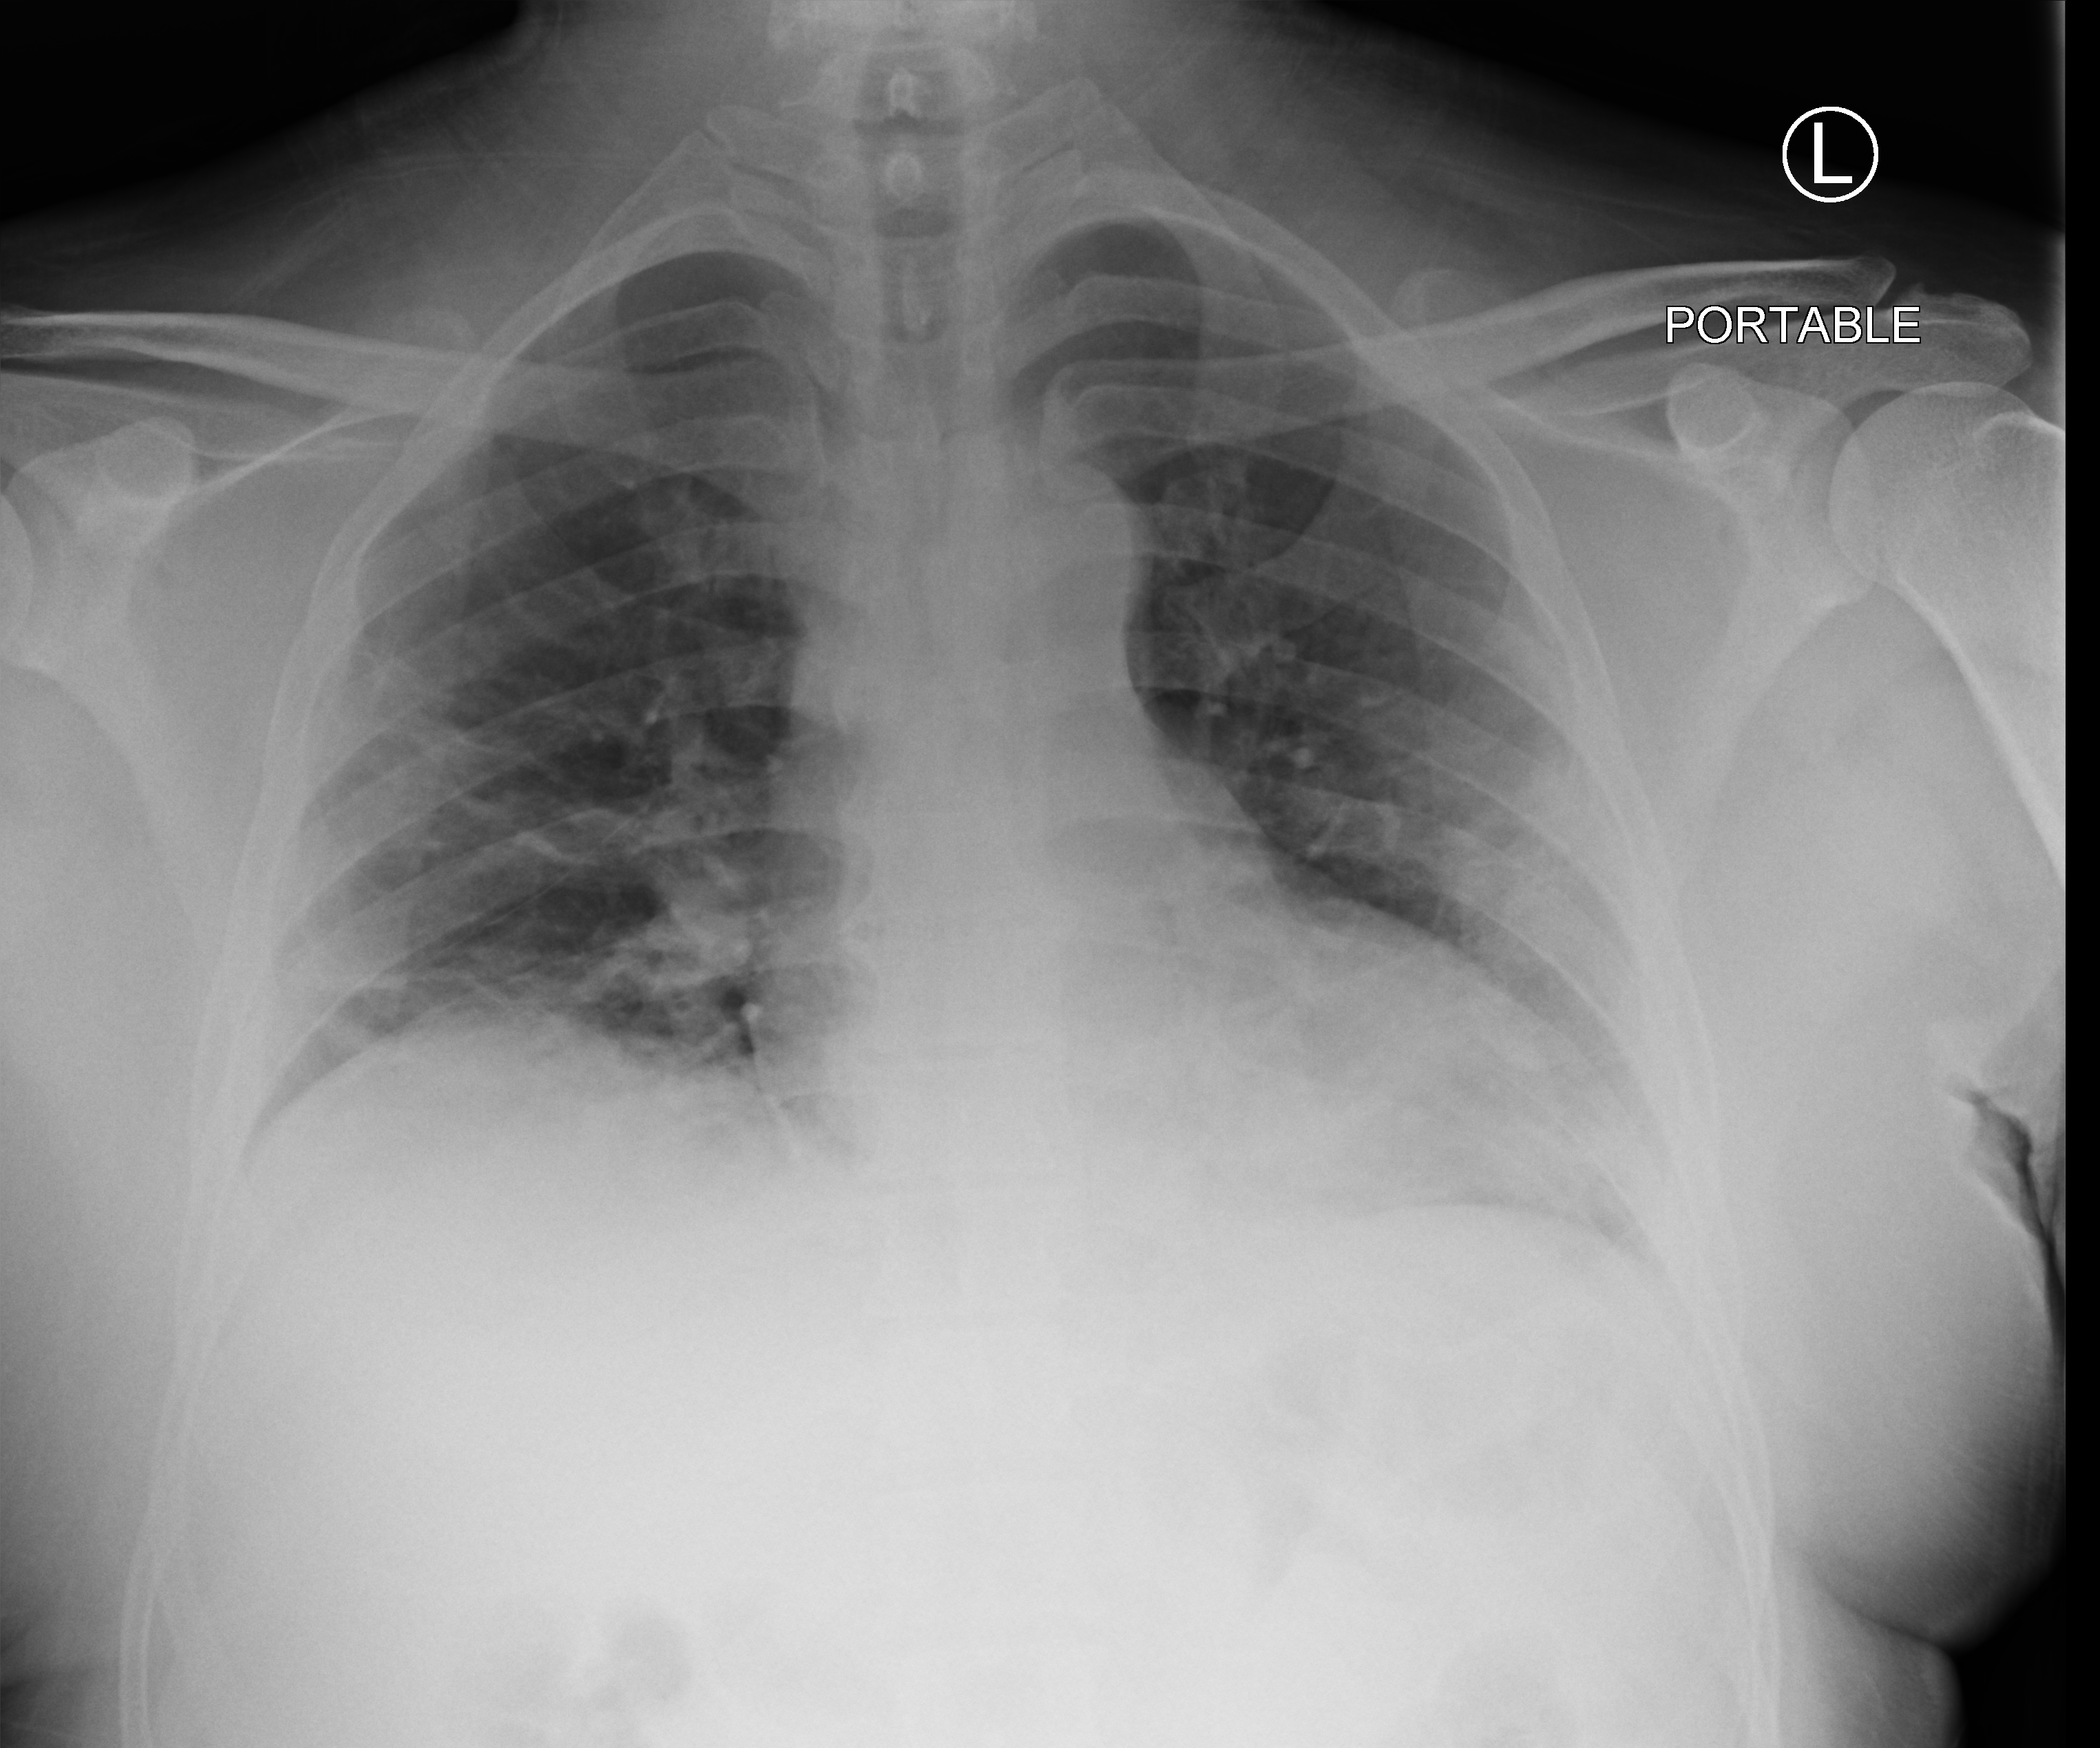
Portable chest radiograph, anteroposterior (AP) projection. Patient hospitalised with COVID-19; male, aged 18–59 years.
Hospital-stay facts (about this admission, not read from this image; timing relative to this image not recorded): mechanically ventilated during this hospital stay: no; admitted to intensive care during this hospital stay: no.